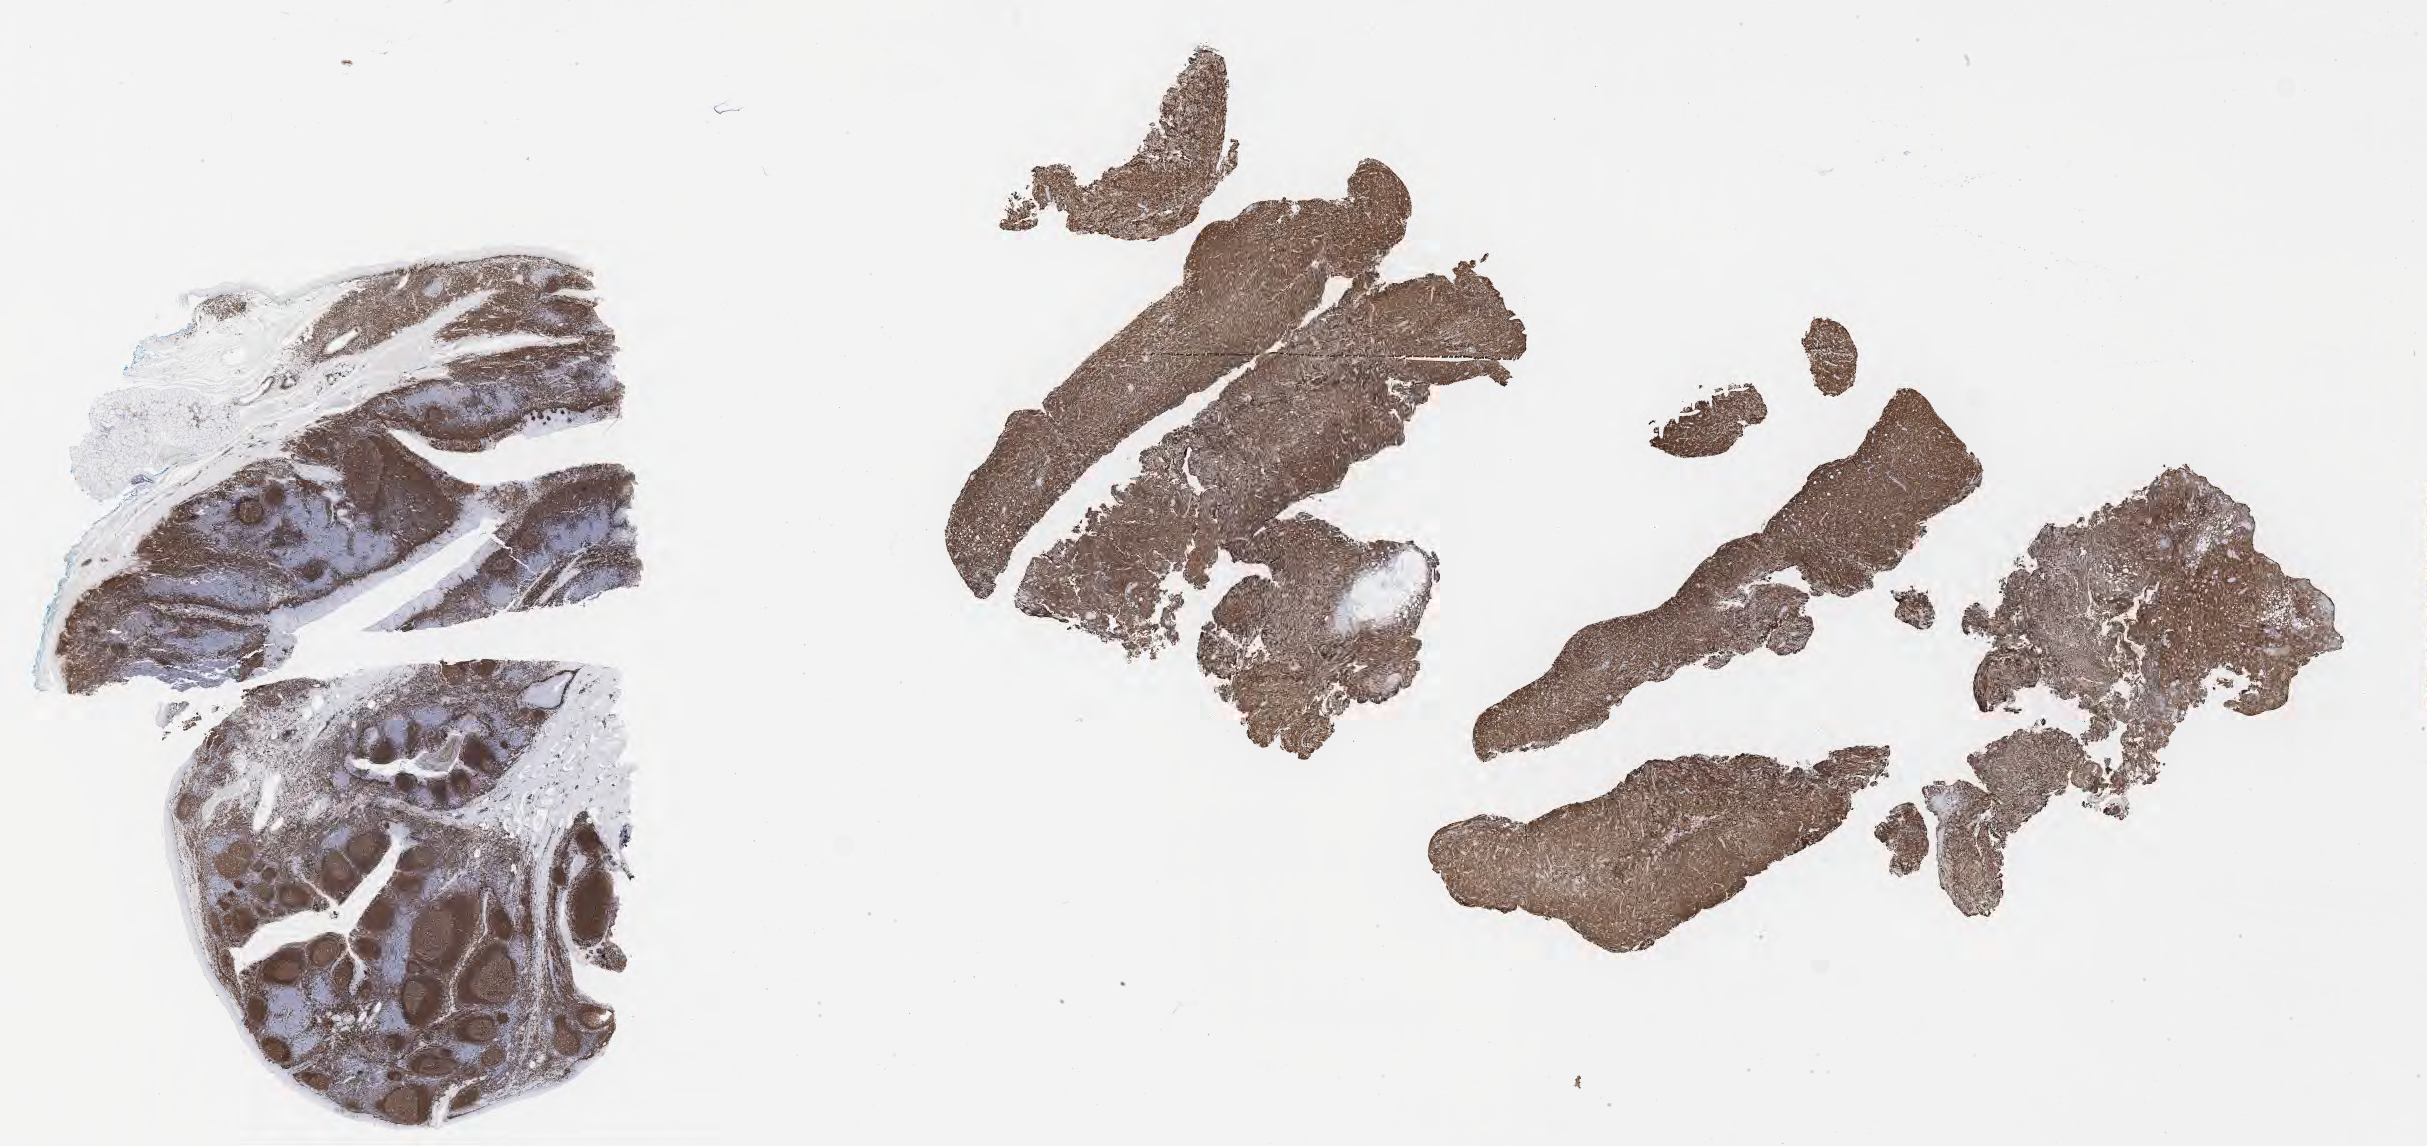
Immunohistochemistry (IHC) whole-slide image stained for CD79a — a low-resolution overview of the entire scanned area, about 39.2 x 18.5 mm, tumor tissue. Male patient, aged 45.
- diagnosis: Diffuse large B-cell lymphoma, NOS